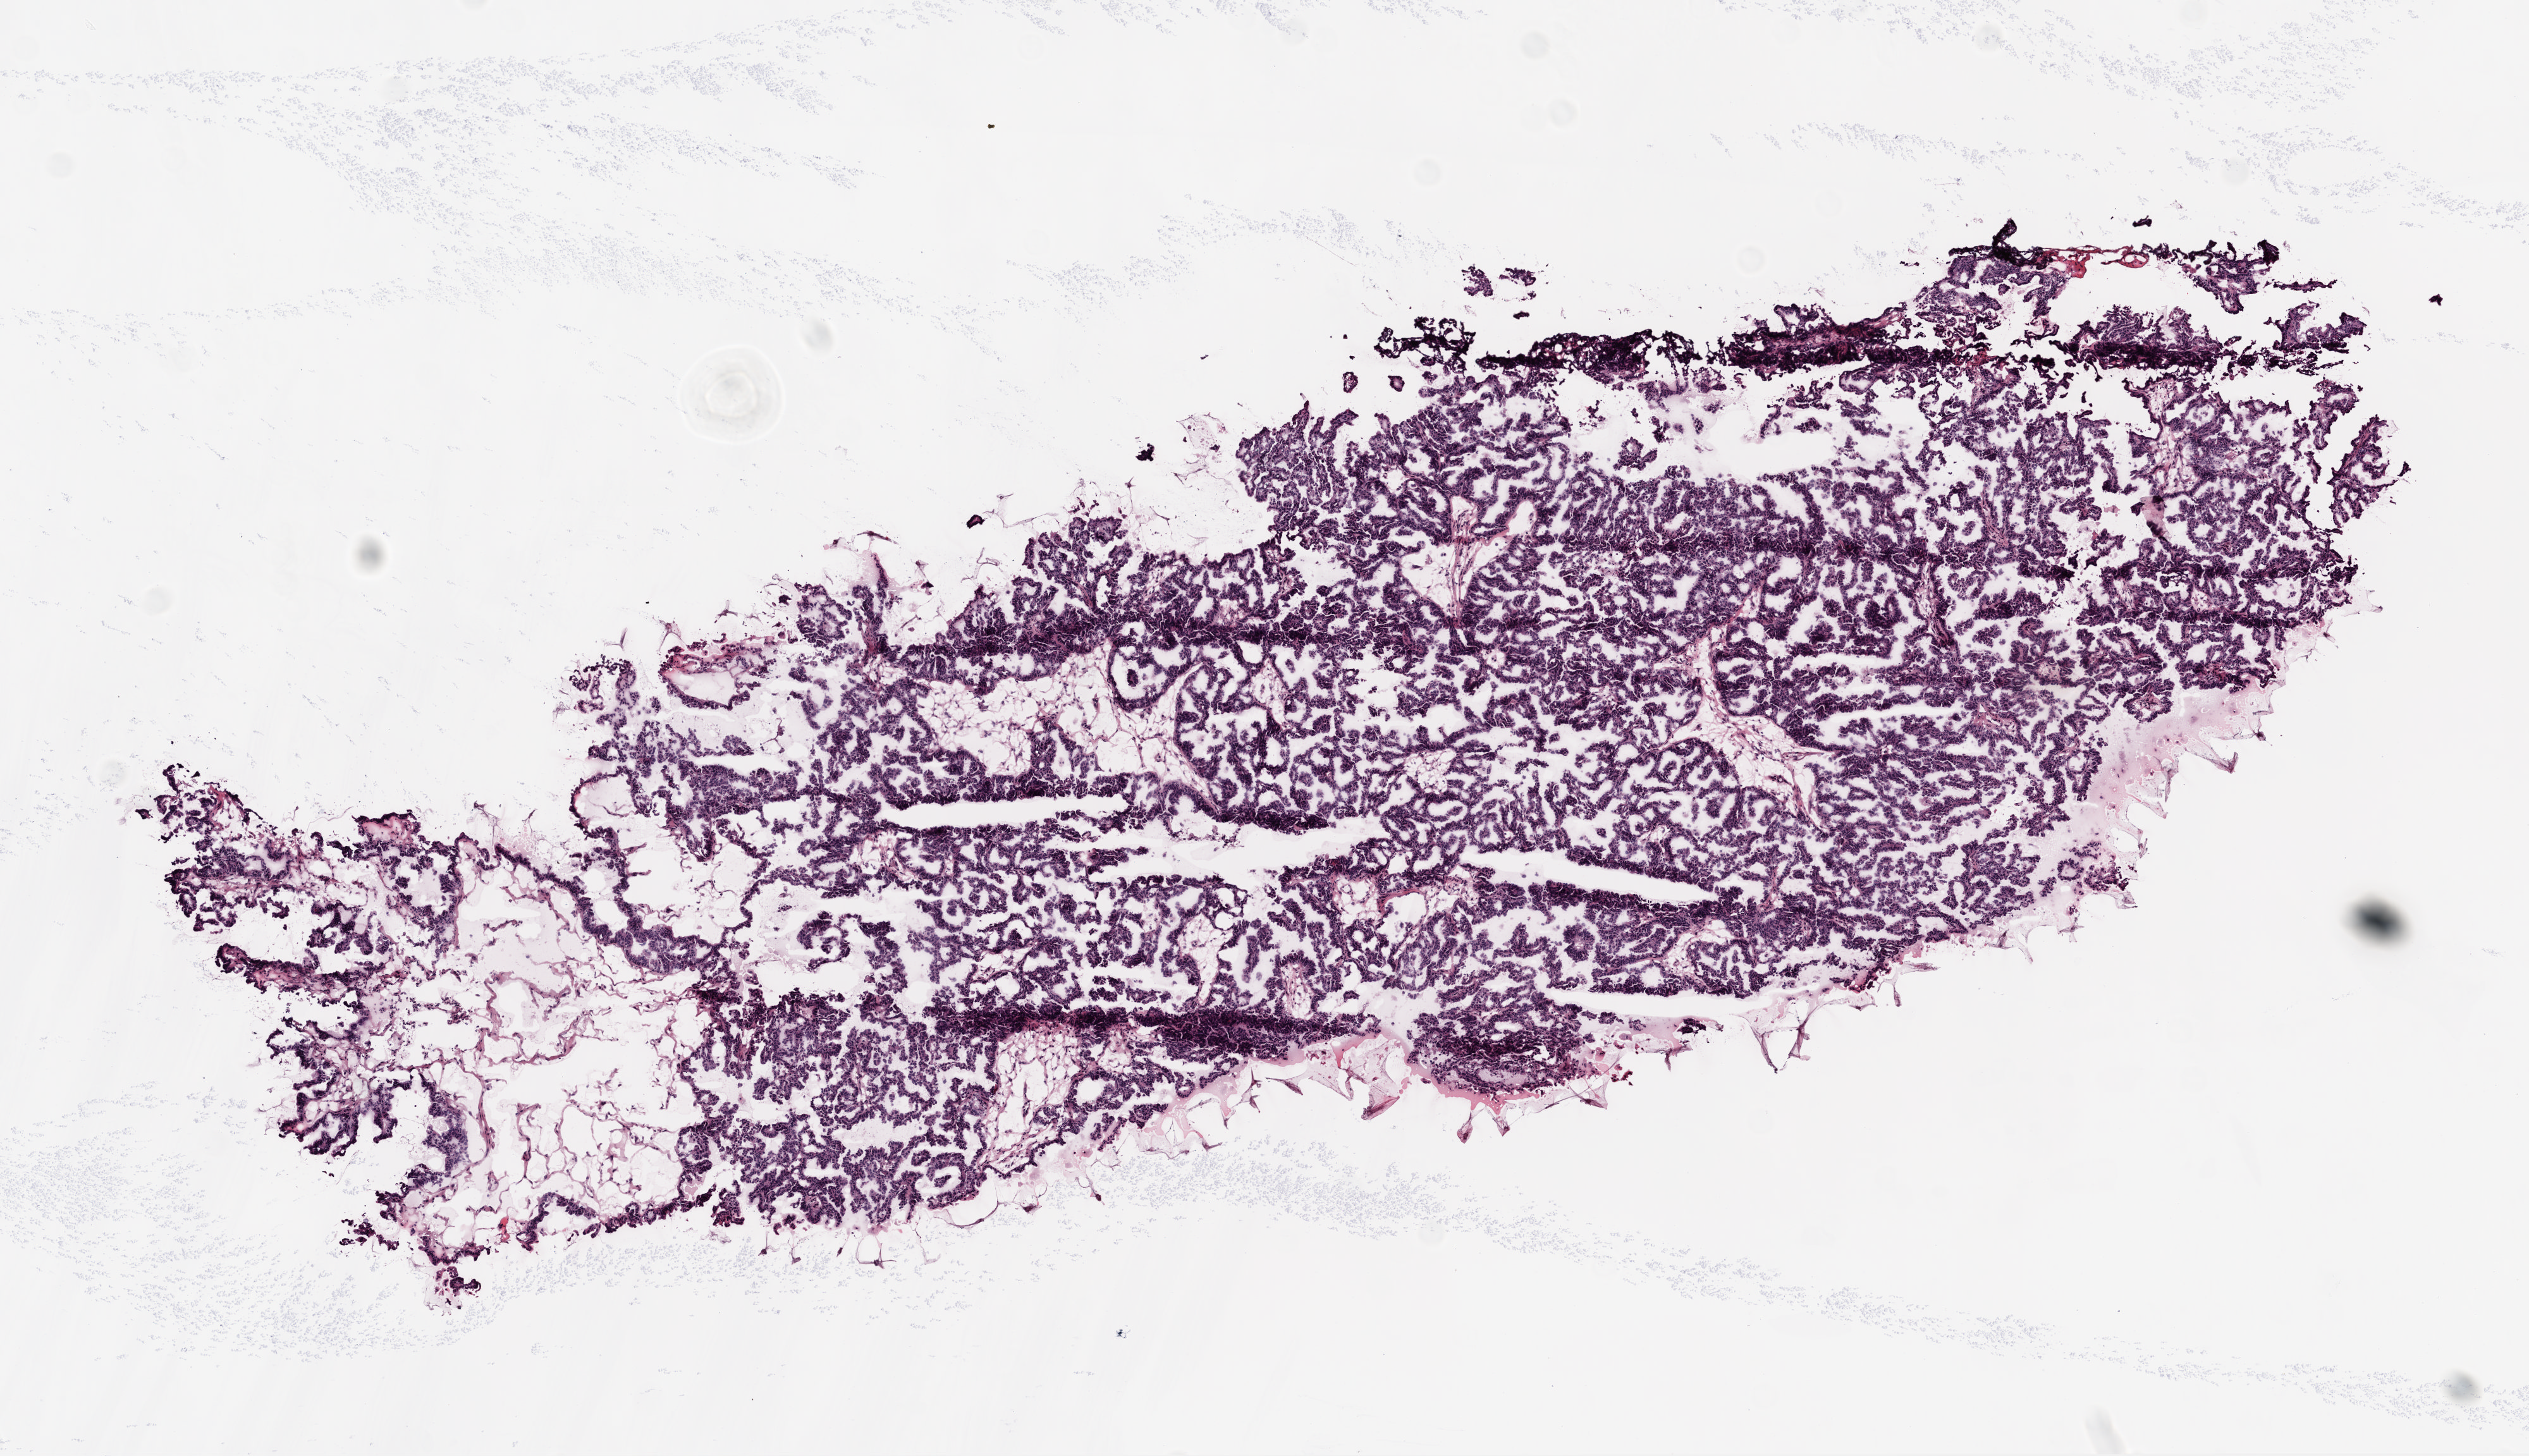
Digitized Hematoxylin and eosin (H&E) stained tissue section (whole slide), a low-resolution overview of the entire scanned area, about 8.0 x 4.6 mm (from a 20x scan); frozen section; primary tumour sample from the ovary. Patient: female, age at initial diagnosis 43 years. Histologic grade: G2 (moderately differentiated). Composition of this section per pathologist review: tumour cells 100%, tumour nuclei 95%, normal cells 0%, stromal cells 0%, necrosis 0%.
FIGO stage: IIIC. Histologic diagnosis: Serous cystadenocarcinoma, NOS.